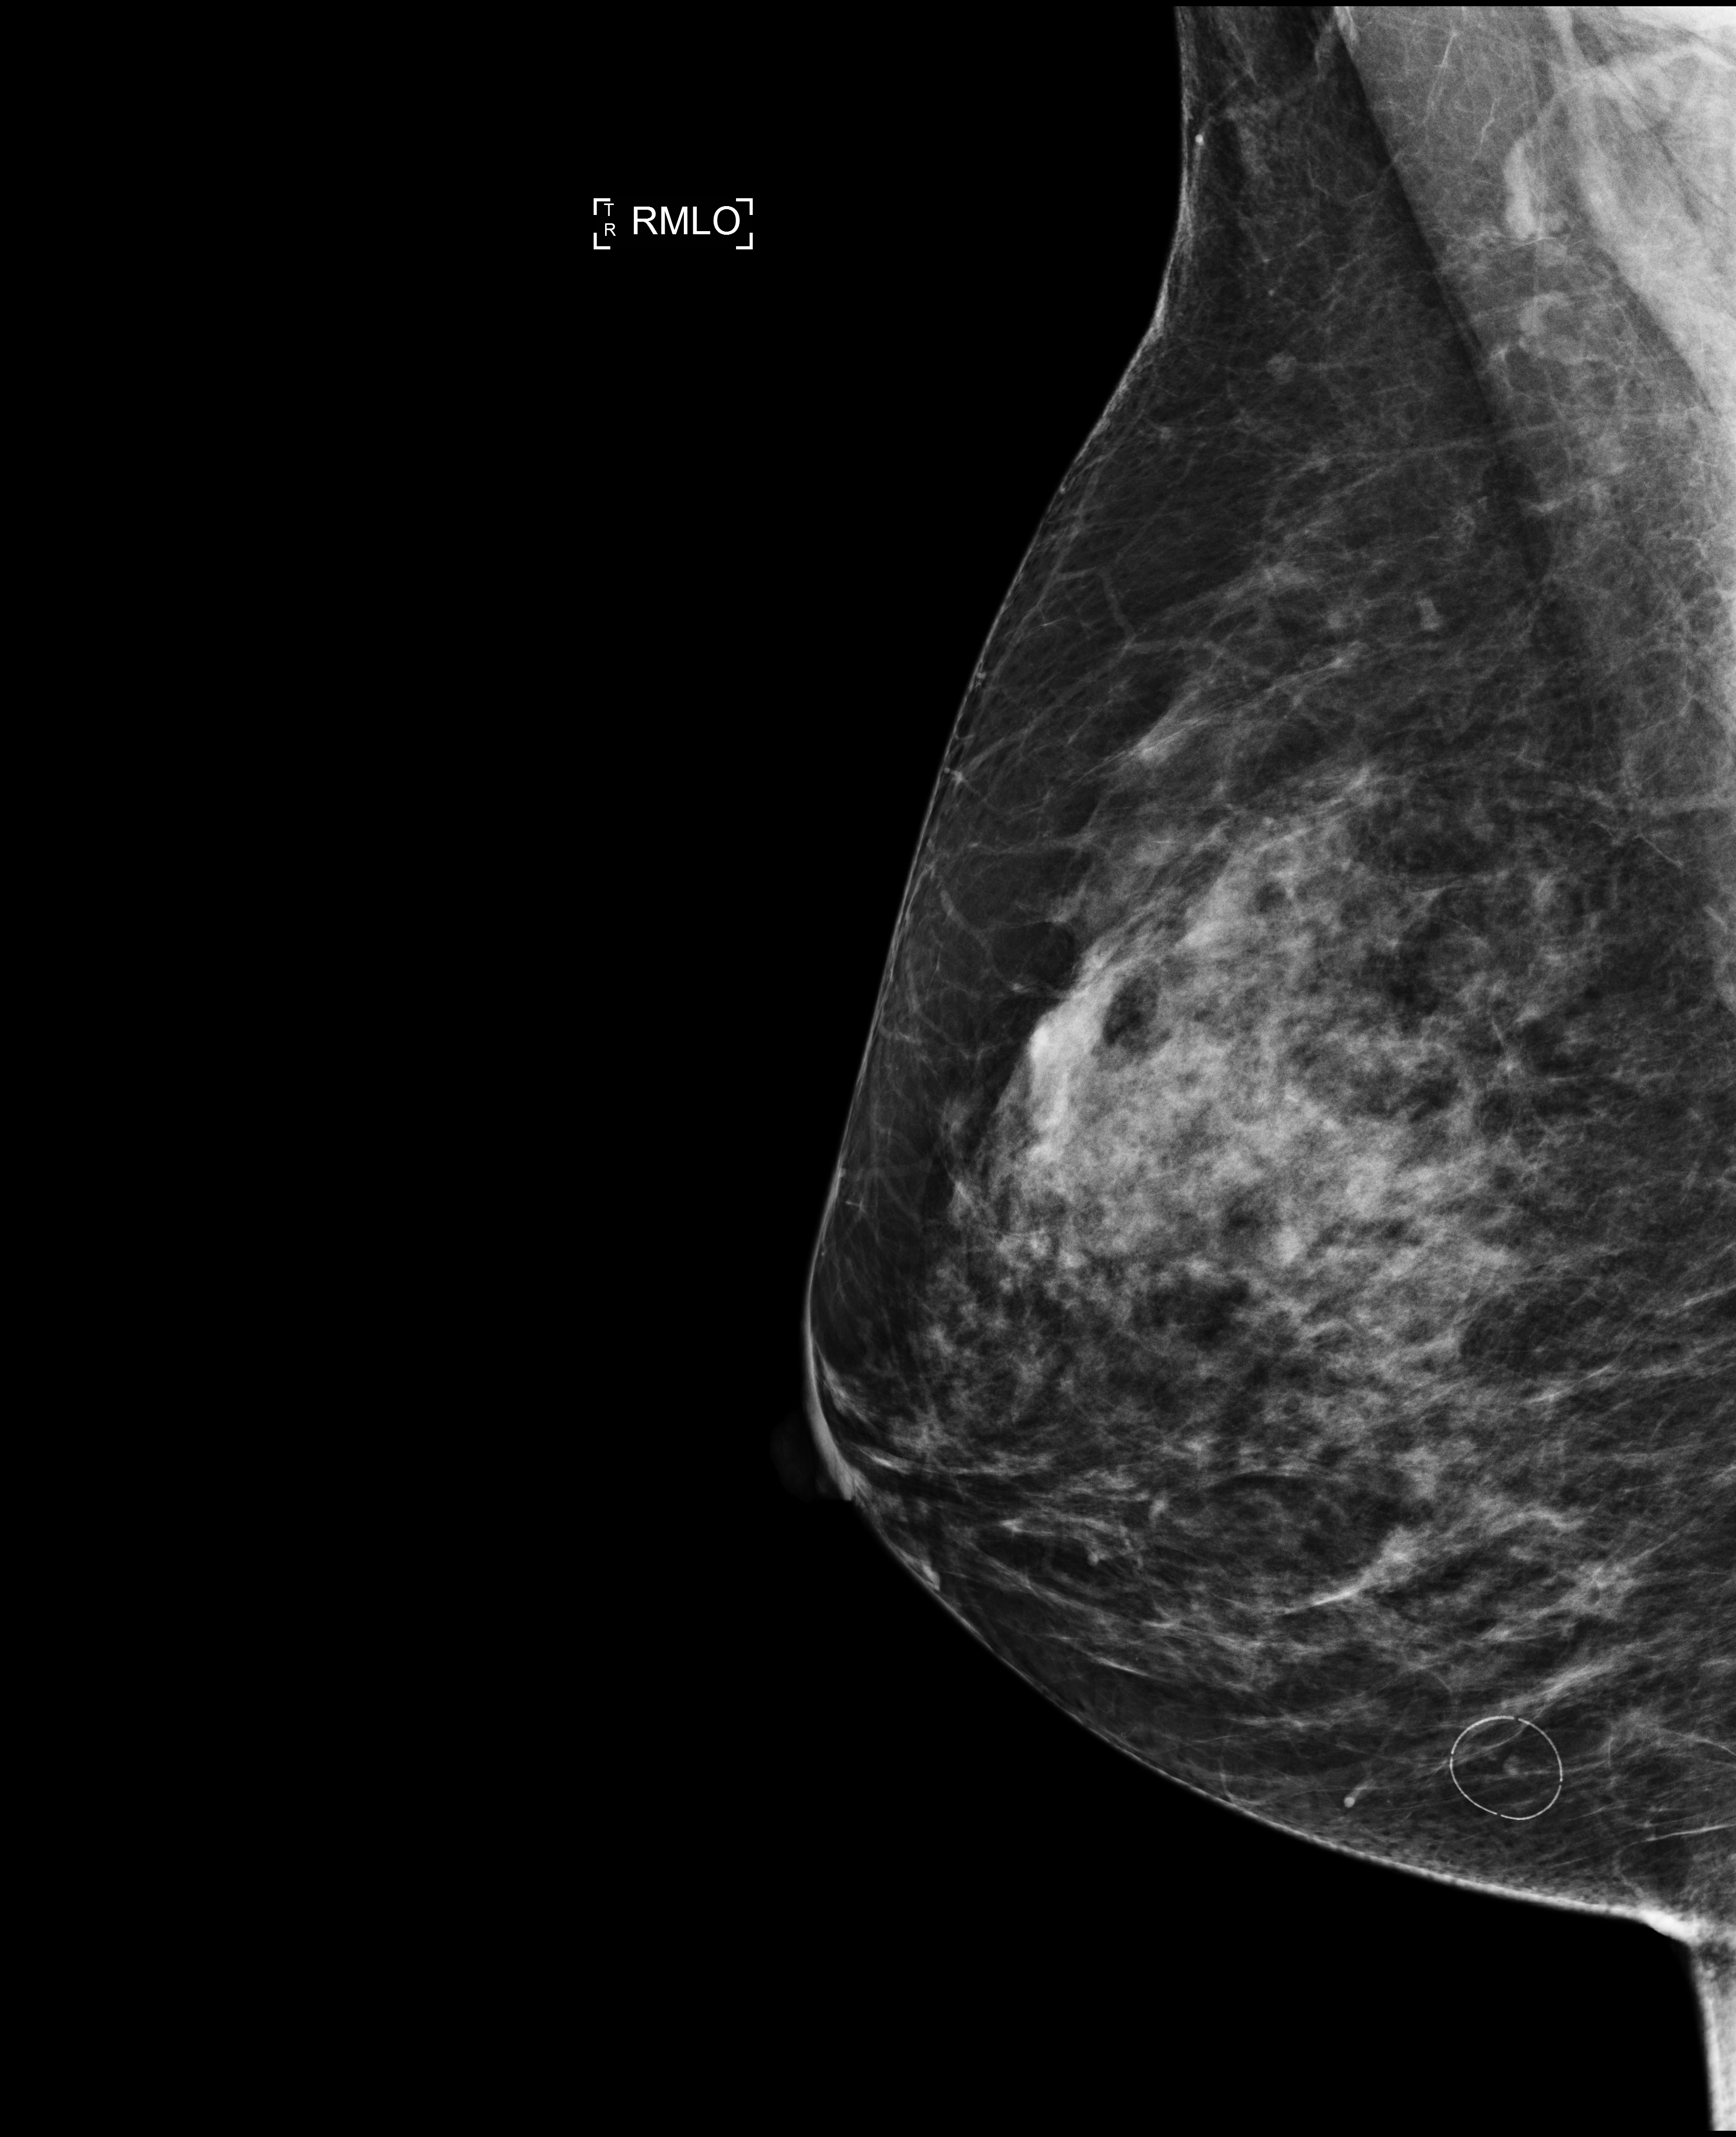
Digital mammogram (FFDM); right breast; MLO view; annual screening mammography examination. Patient: female, 46 years.
- BI-RADS breast density category at the screening exam (both breasts, scale 1–4): 3
- final BI-RADS assessment for this screening round (tomosynthesis exam, both breasts): category 1
- recall: no recall after this screen